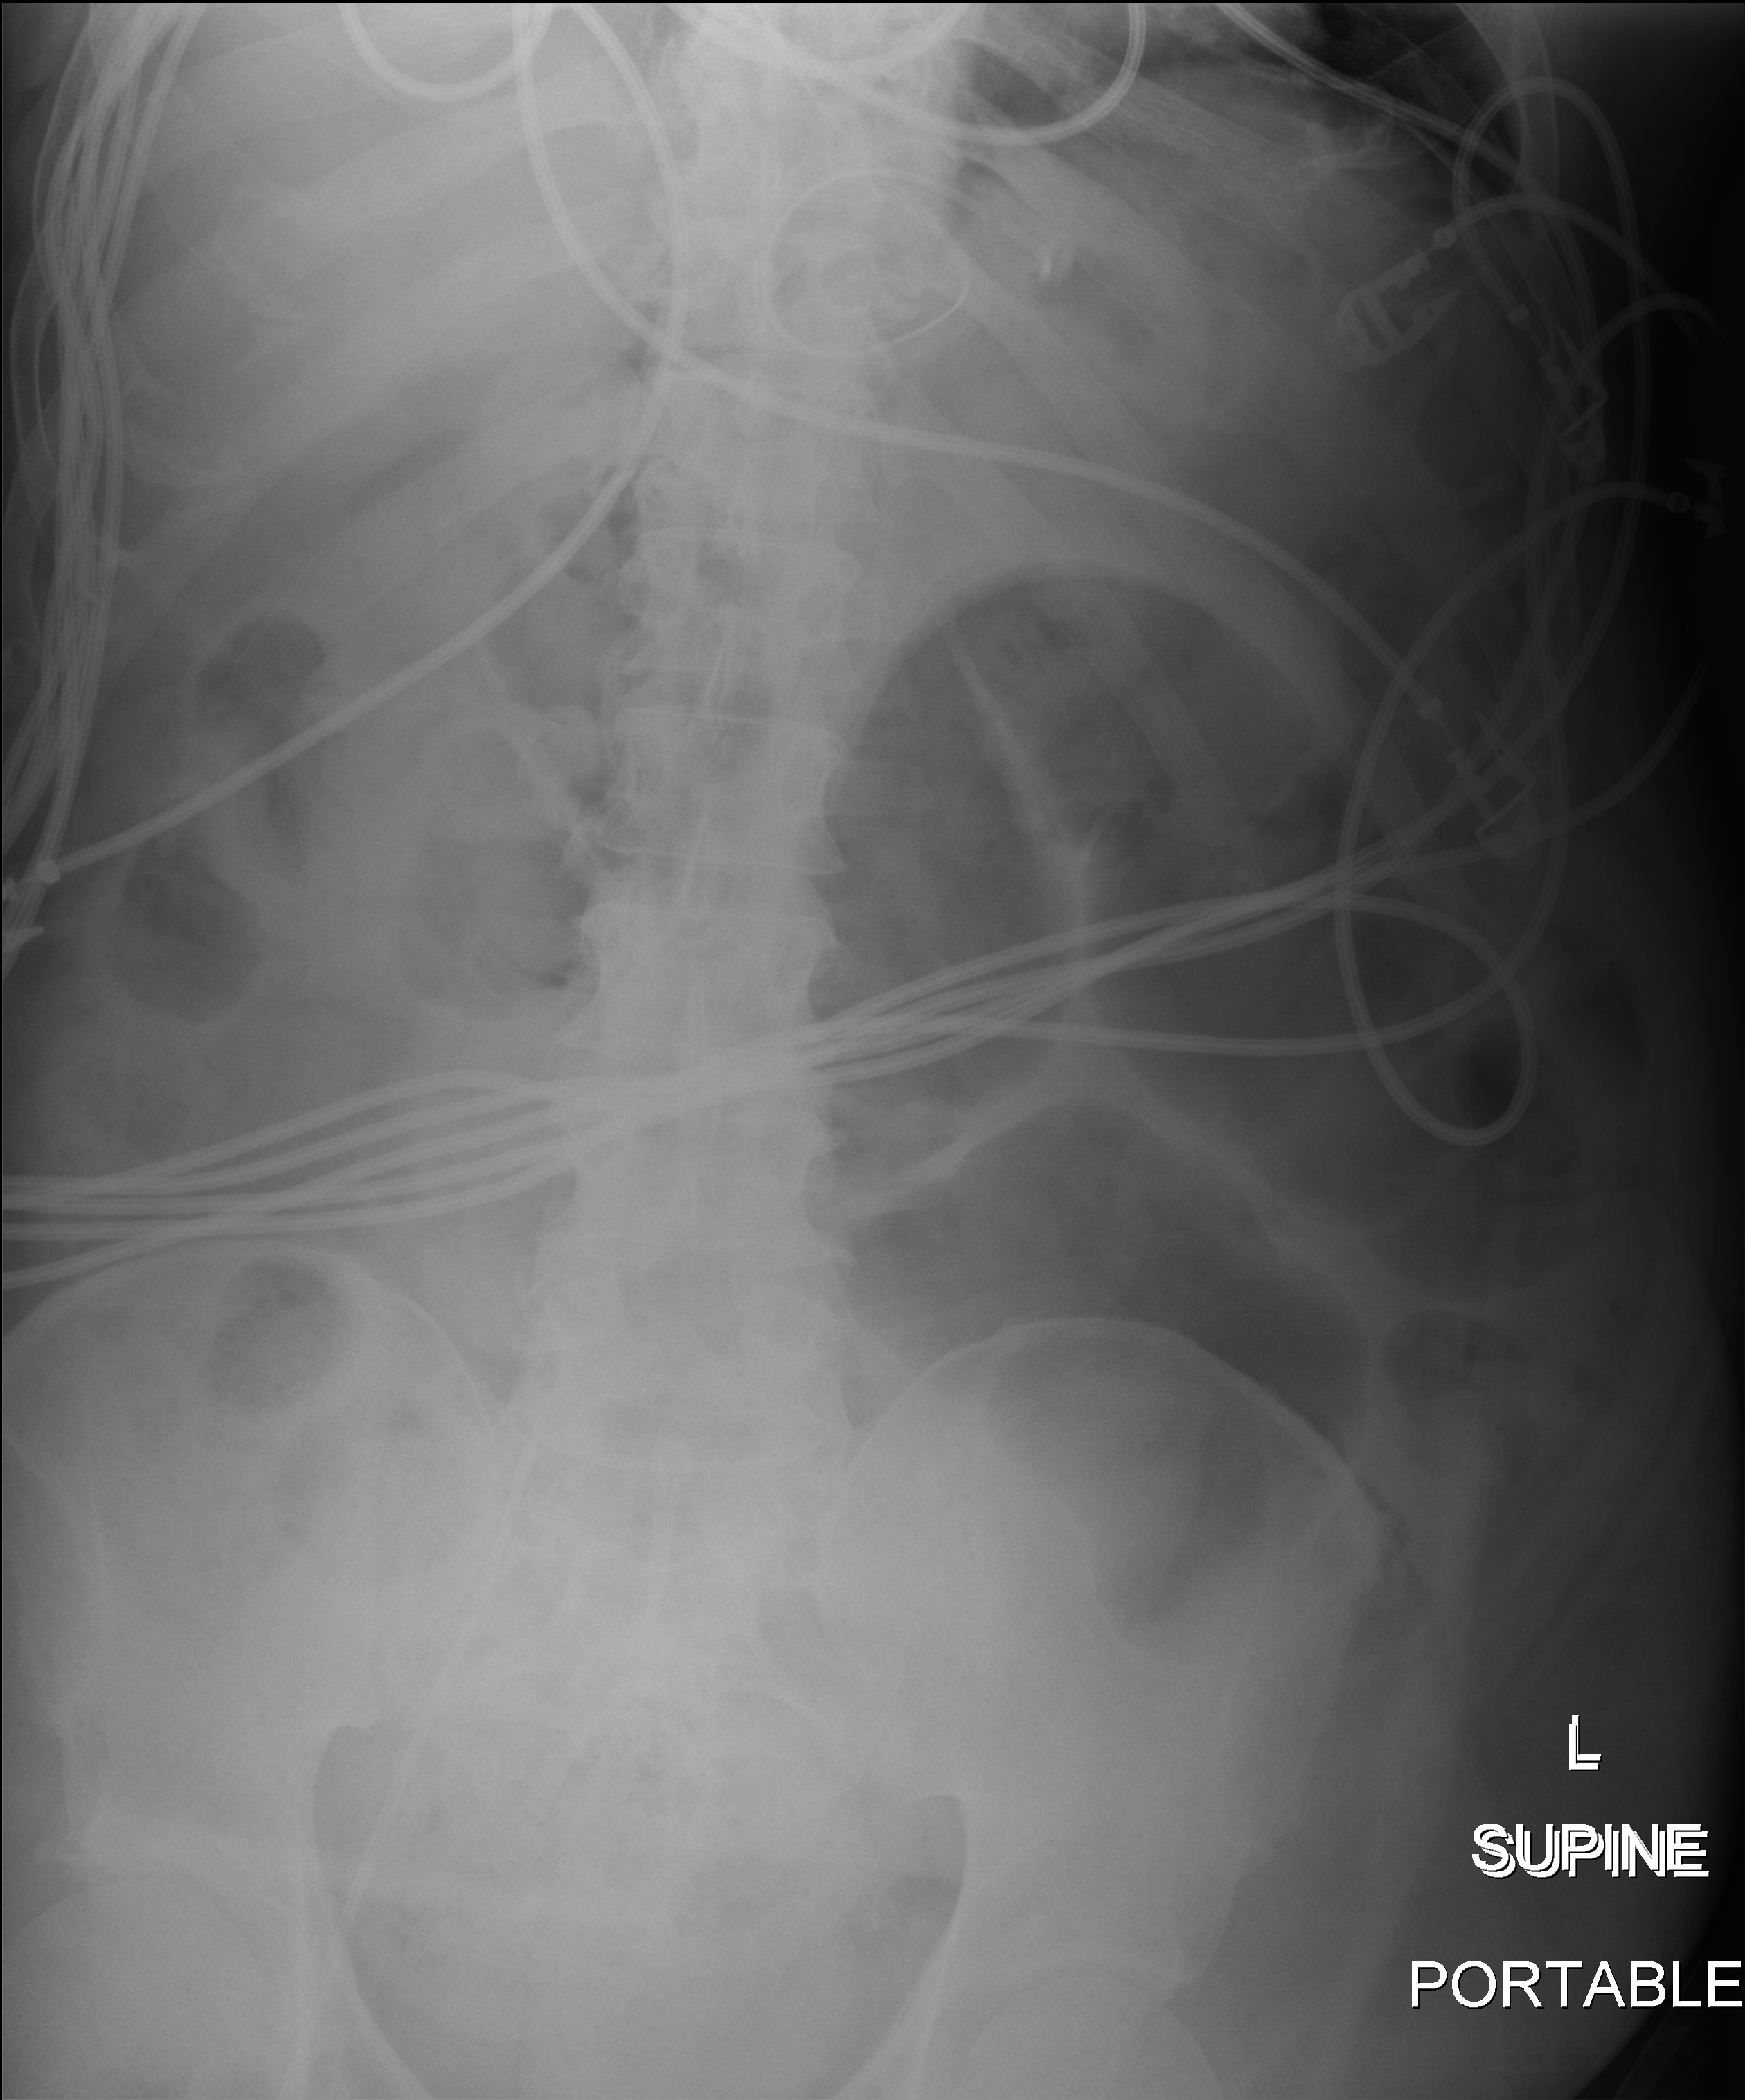
Bedside abdomen radiograph (digital radiography). Adult patient hospitalised with COVID-19, age 18–59 years.
Hospital-stay facts (about this admission, not read from this image; timing relative to this image not recorded):
- chronic kidney disease (admission record): no